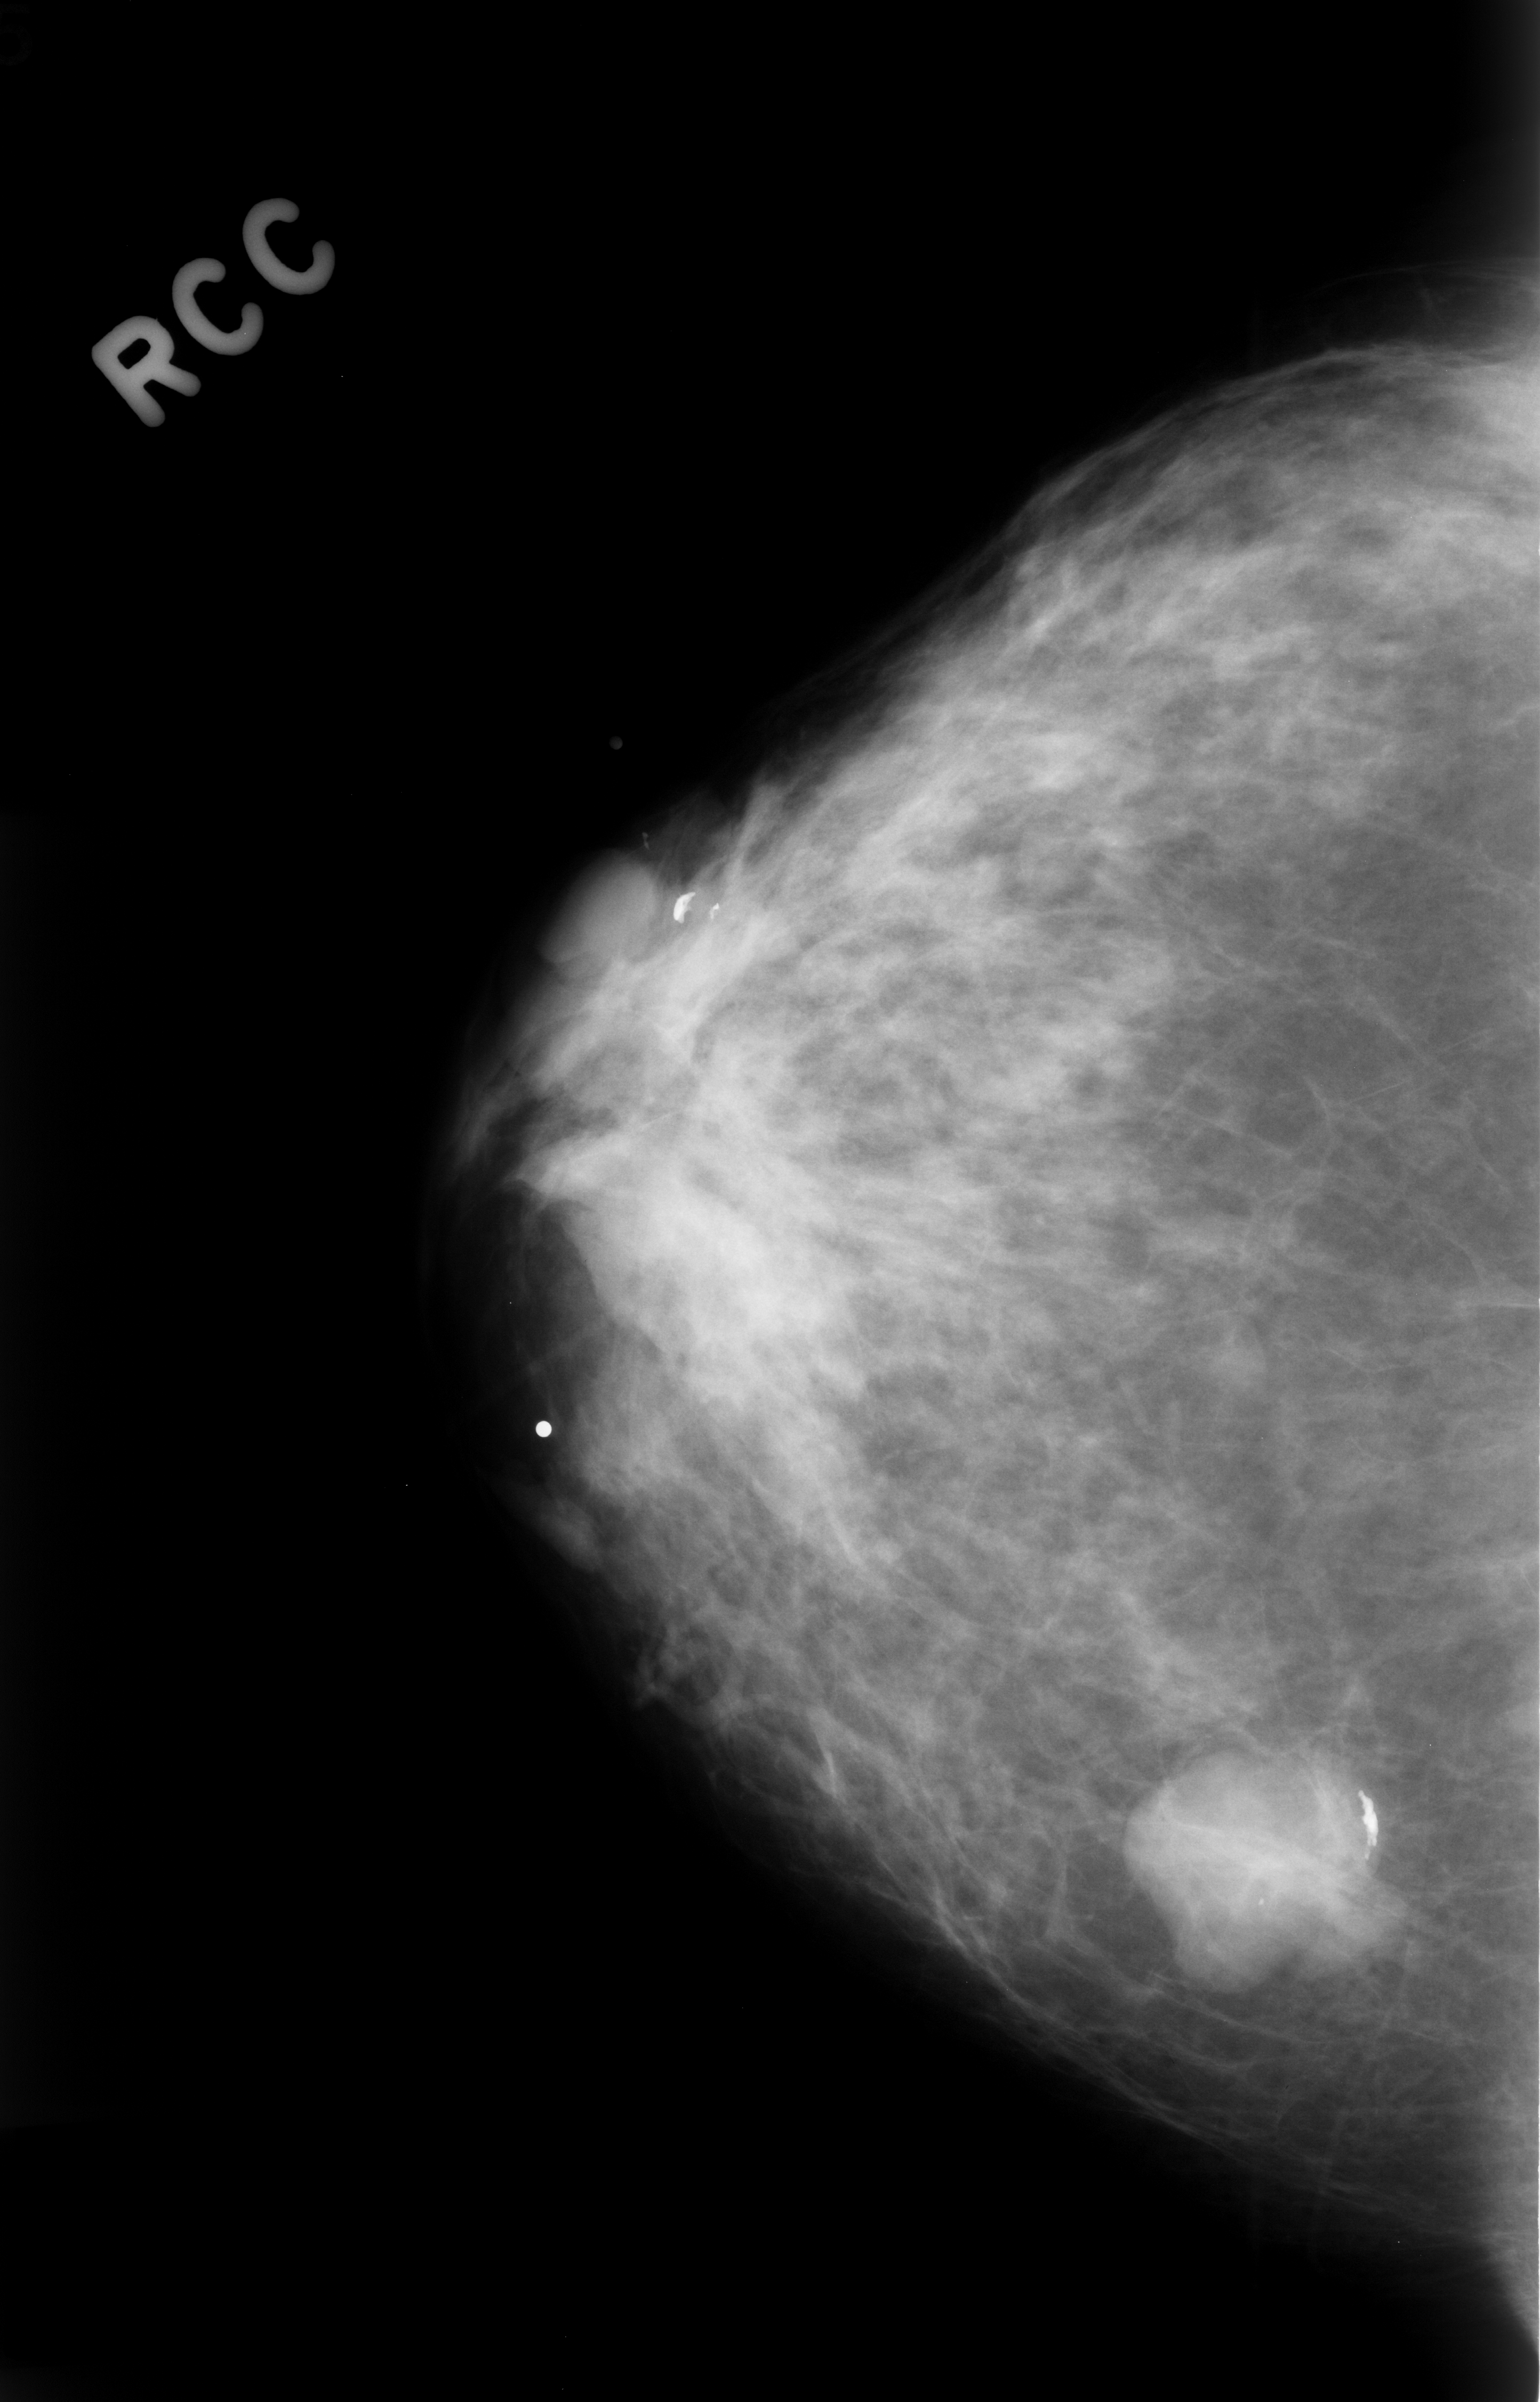
Mammogram (digitized film); right breast; craniocaudal (CC) view; breast composition: scattered fibroglandular densities (BI-RADS density category 2 of 4).
Abnormality record for this image: Finding 1 of 4: mass, shape oval, margins circumscribed; BI-RADS assessment category 3; pathology result (as recorded, not read from the image): benign. Finding 2 of 4: mass, shape oval, margins circumscribed; BI-RADS assessment category 3; subtlety rating 5 on a 1 (subtle) to 5 (obvious) scale; pathology (as recorded): benign. Finding 3 of 4: mass, shape oval, margins circumscribed; BI-RADS assessment category 3; subtlety rating 5 on a 1 (subtle) to 5 (obvious) scale; pathology (as recorded): benign. Finding 4 of 4: mass, shape lobulated, margins circumscribed; BI-RADS assessment category 3; pathology (as recorded): benign.